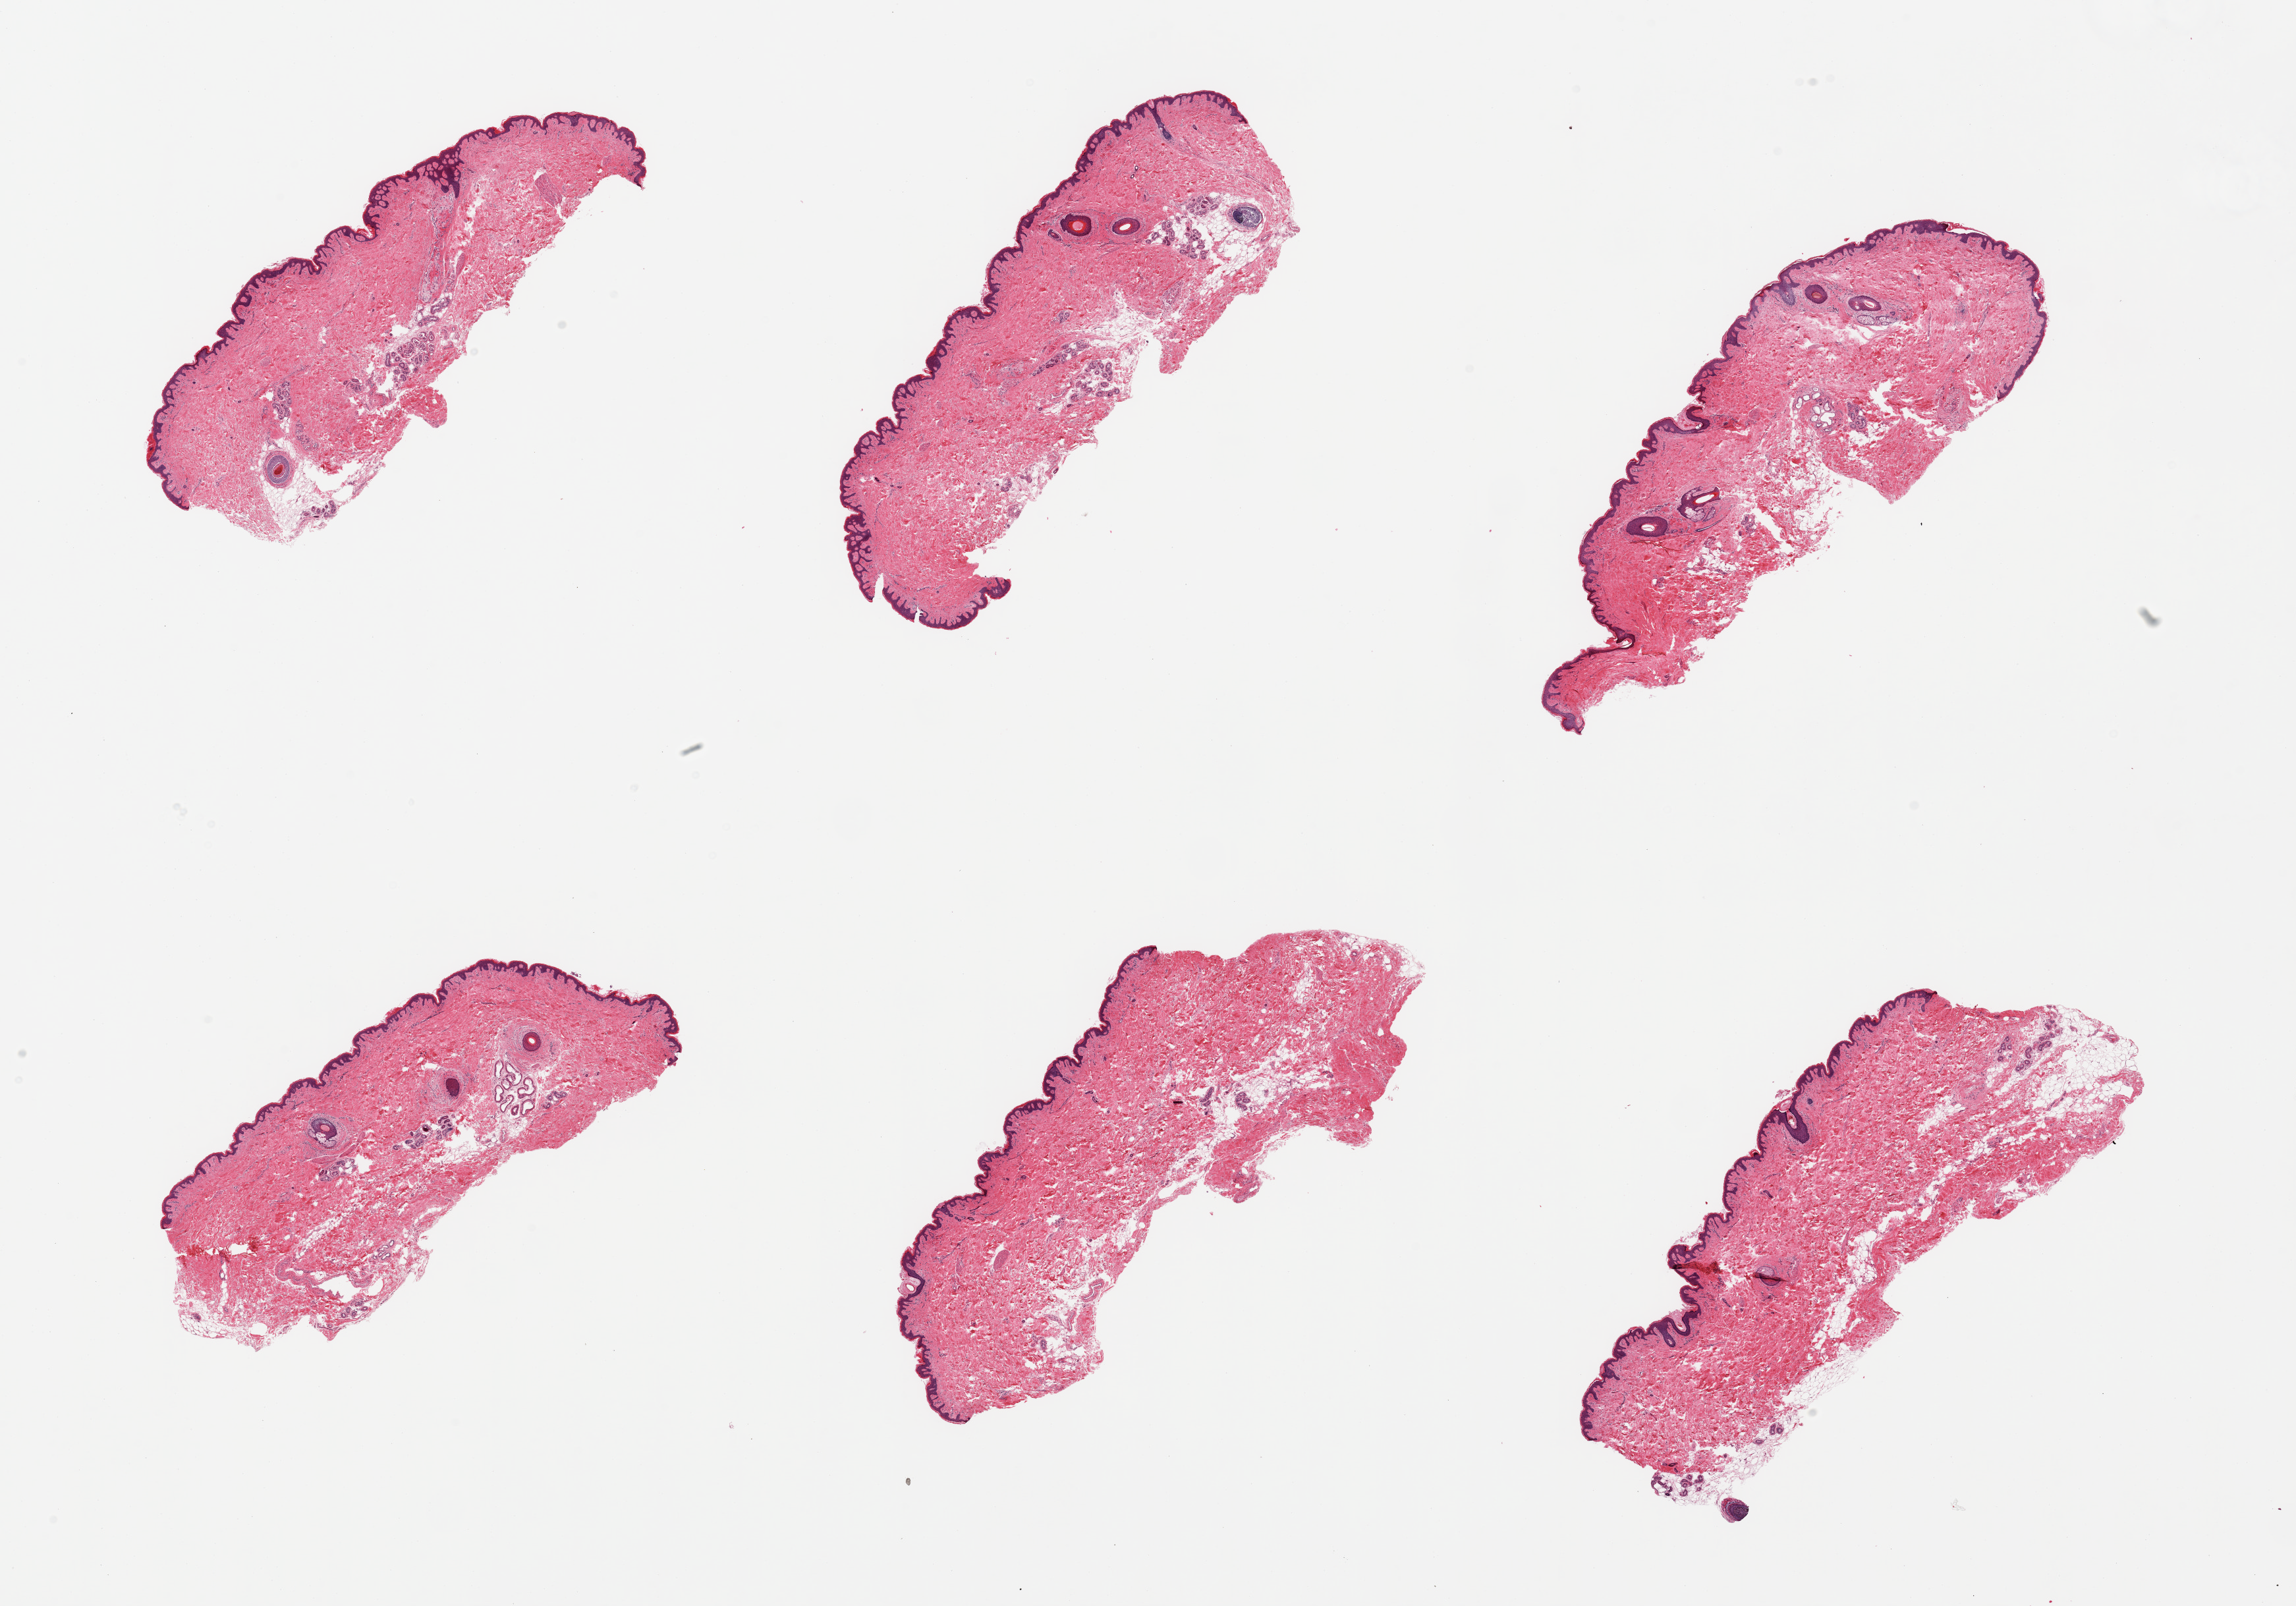
Haematoxylin and eosin whole-slide image, brightfield — whole scanned area (about 27.6 x 19.3 mm, from a 20x scan) shown as a low-resolution overview, PAXgene-fixed paraffin-embedded (PFPE) section, target tissue: skin of suprapubic region, donor tissue sample. Male donor.
Pathologist's review note for this sample: 6 pieces; ~10% internal fat (periadnexal).